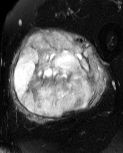
MRI of an extremity soft-tissue mass, one axial slice; T2-weighted fat-saturated; MR volume resampled by the dataset authors to the PET/CT grid (not the native acquisition matrix); 123 × 153 image matrix, field of view 120 × 149 mm. Male patient. Case-level facts recorded for this patient, not image findings: histological type: pleiomorphic liposarcoma; grade: high; site of the primary tumour: left thigh.
Outlined on this slice (expert contour drawn on MRI and transferred to this co-registered scan by the dataset authors):
- gross tumour volume including surrounding oedema: box from (x=9, y=27) to (x=110, y=124) px
- gross tumour volume (mass): (x=13, y=31)–(x=96, y=117)